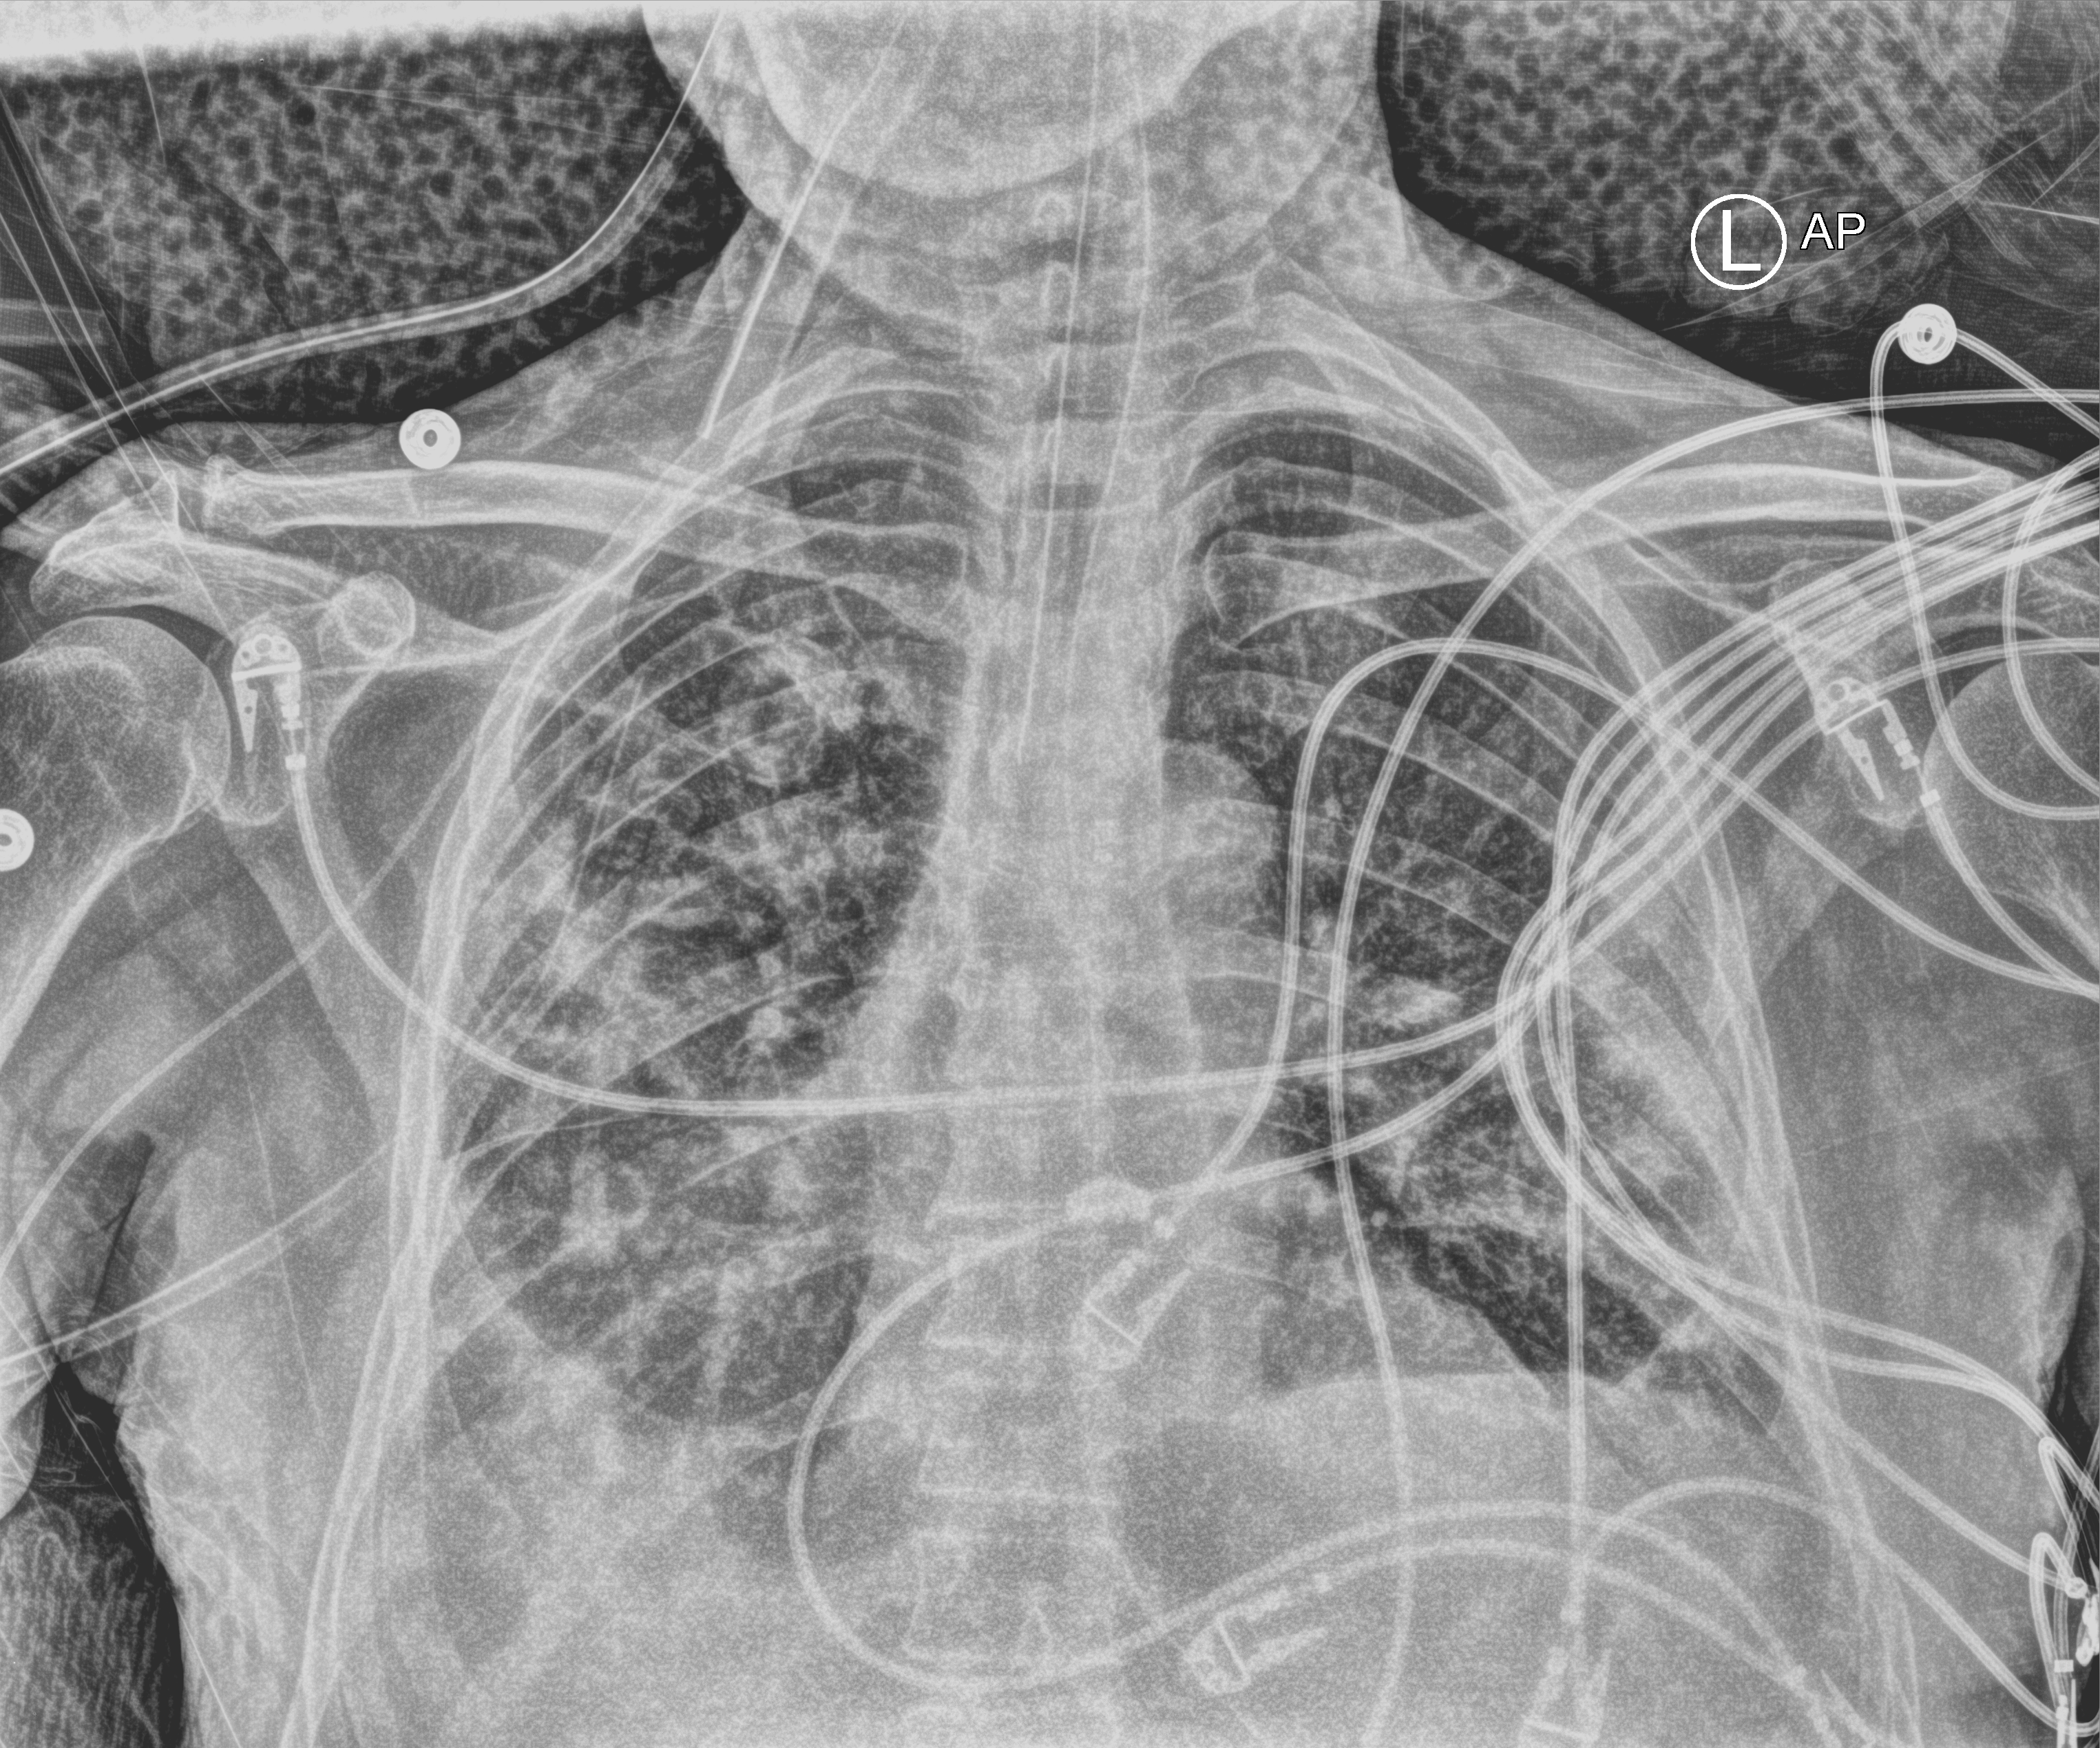
Bedside chest radiograph (computed radiography), anteroposterior (AP) projection. Male patient hospitalised with COVID-19, age 75–90 years.
Hospital-stay facts (about this admission, not read from this image; timing relative to this image not recorded):
- mechanically ventilated during this hospital stay: yes
- smoking status (admission record): never
- other chronic lung disease (admission record): yes